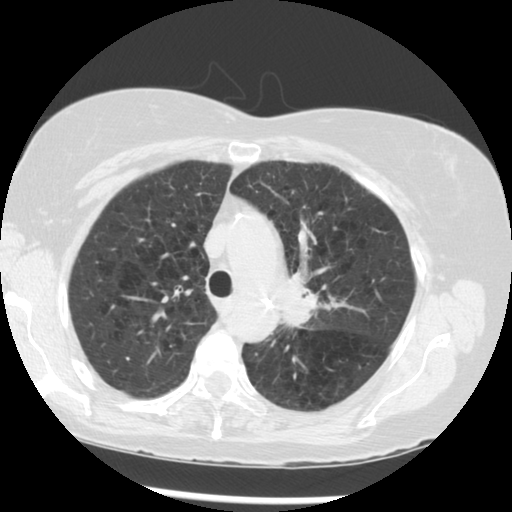
Low-dose screening chest CT, axial slice. Third screening round (two years after baseline). Lung window (W 1500 / L -600 HU). 2.5 mm slice thickness. 120 kVp. Slice 209 of 283 in the series. 512 × 512 image matrix, field of view 330 × 330 mm. Female participant, aged 70 years at enrolment. Current smoker at enrolment.
• Expert reader's lesion annotation, bounding box <270,262,363,352> (left, top, right, bottom; pixels).
• The exam's reader record, not a measurement of the box and not confirmed to be the same lesion: non-calcified nodule or mass ≥4 mm, left upper lobe, 32 × 26 mm, spiculated (stellate) margins, soft tissue attenuation, pre-existing on the prior screen: yes; interval growth: yes.
• Lung cancer was diagnosed 24 days after this screen: neoplasm, malignant, left upper lobe, stage IIIB (AJCC 6th edition), 40 mm at pathology.